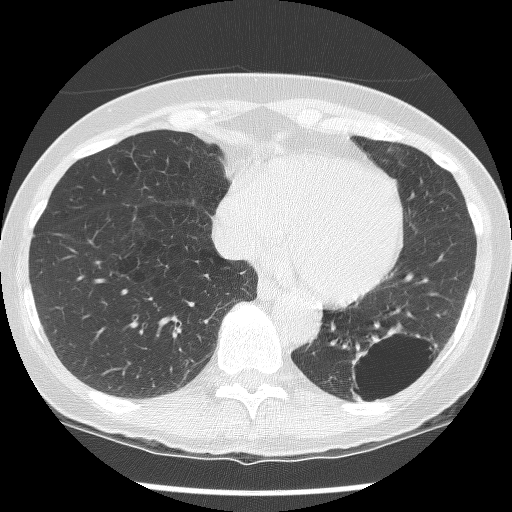
Axial slice from a low-dose chest CT screening exam; second annual screen; lung window (W 1500 / L -600 HU); 2.5 mm slice thickness; slice 93 of 136 in the series. Female, age 61 years at enrolment. Current smoker at enrolment.
• Lesion marked by an expert reader, bounding box [x1, y1, x2, y2] px = [331, 323, 437, 415].
• The screening reader recorded 2 non-calcified nodules or masses ≥4 mm on this exam; which of them this box marks is not recorded.
• Lung cancer was diagnosed 585 days after this screen (after the third annual screen): non-small cell carcinoma, left lower lobe, poorly differentiated (G3), stage IB (AJCC 6th edition), 100 mm at pathology.